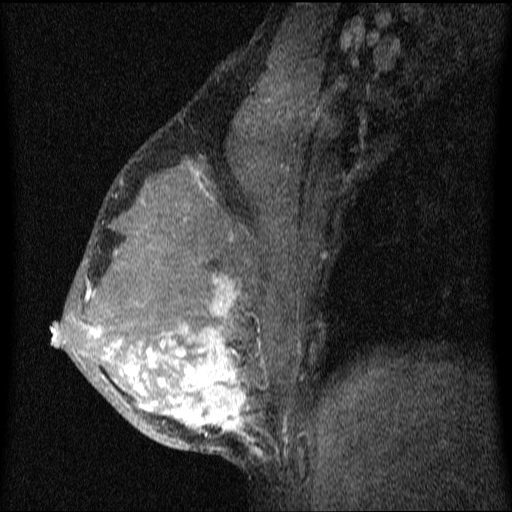
Breast MRI (dynamic contrast-enhanced), one sagittal slice. Slice 41 of 64 in the series (ordered by position). Dynamic contrast-enhanced series, image 2 of 4 at this slice position (ordered by acquisition). 1.5 T. TE 4.2 ms, TR 9.1 ms. 2 mm slice thickness. 512 × 512 image matrix, field of view 180 × 180 mm. Patient: female, 33 years.
Structures marked on this image (semi-automatically segmented with operator editing):
- analysis volume of interest (the breast-tissue region the enhancement analysis was run in; not a lesion): bounding box (x1, y1, x2, y2) in pixels: (52, 151, 336, 458)
- tumour enhancement mask (voxels above the 70 % enhancement threshold inside the analysis volume of interest): (52, 171, 267, 457)